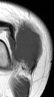
MRI of an extremity soft-tissue mass, one axial slice; slice 21 of 42 in the series (ordered by position); MR volume resampled by the dataset authors to the PET/CT grid (not the native acquisition matrix); 54 × 97 image matrix, field of view 53 × 95 mm. Female patient. Case-level facts recorded for this patient, not image findings: histological type: spindle cell suggestive of biphasic synovial sarcoma; grade: intermediate; site of the primary tumour: left knee.
Structures marked on this image (expert contour drawn on MRI and transferred to this co-registered scan by the dataset authors):
- gross tumour volume including surrounding oedema: bounding box (x1, y1, x2, y2) in pixels: (14, 23, 41, 70)
- gross tumour volume (mass): (14, 25, 41, 70)